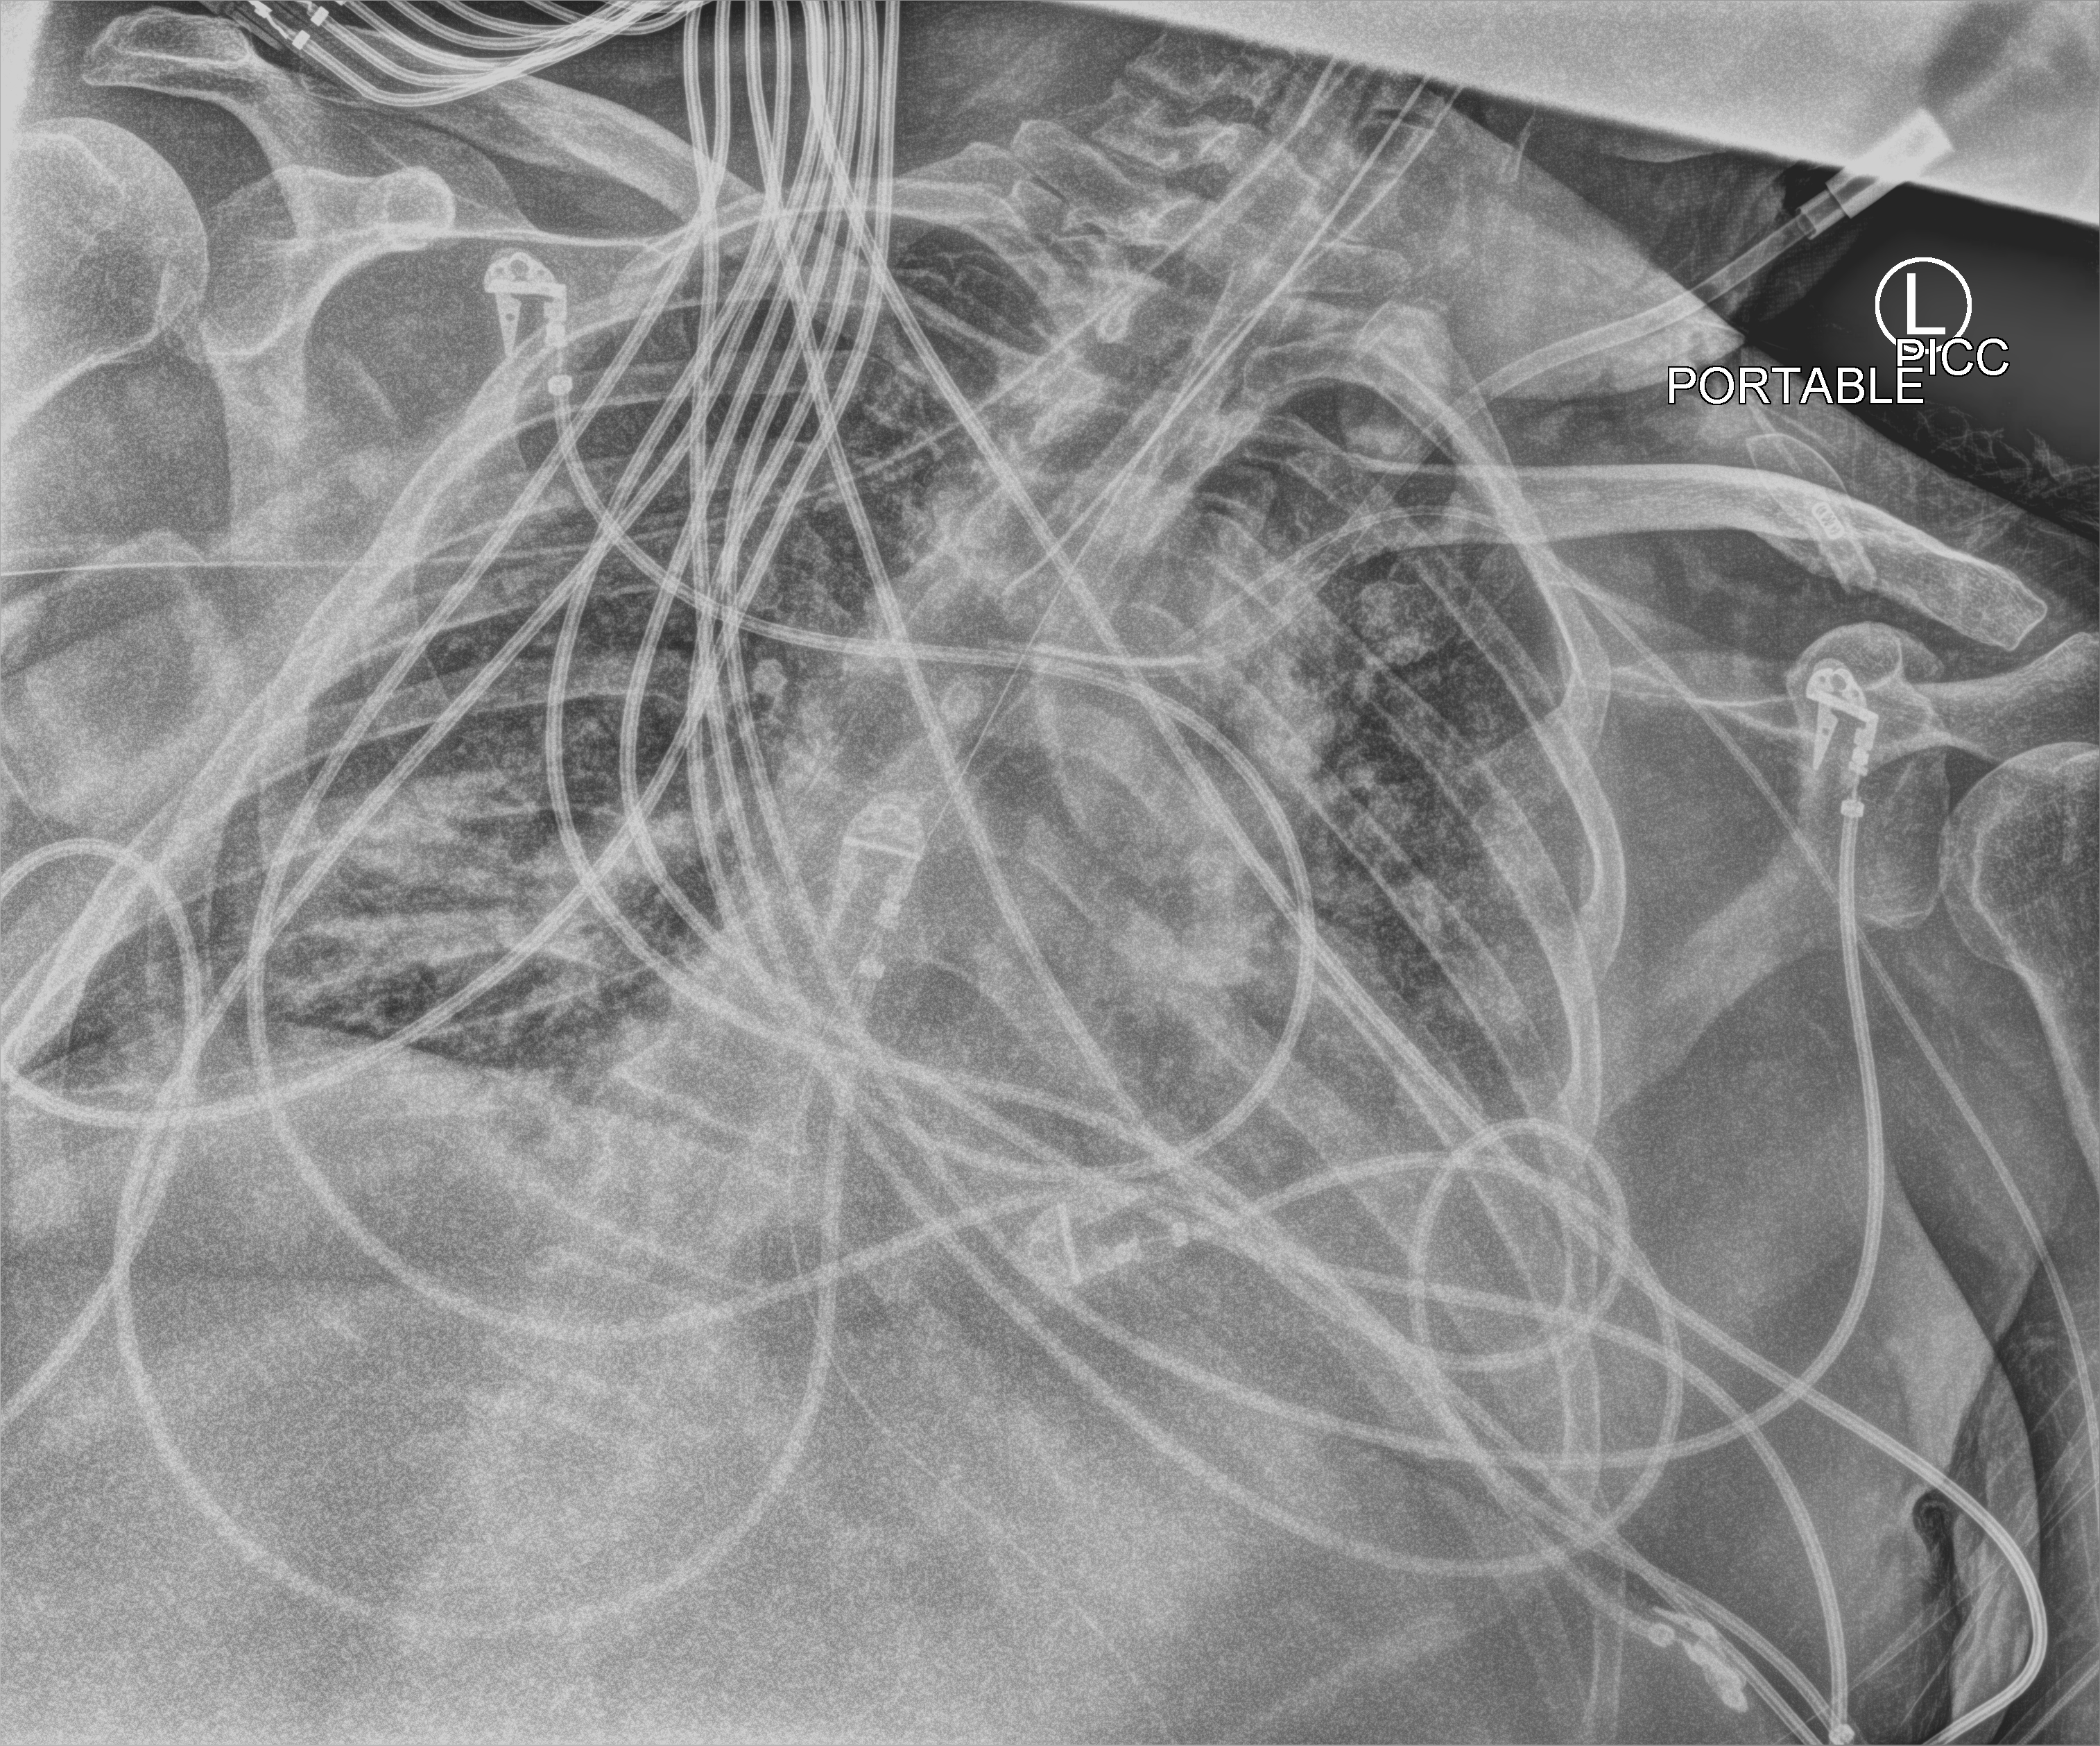
Portable chest radiograph. Male patient hospitalised with COVID-19, age 18–59 years.
Hospital-stay facts (about this admission, not read from this image; timing relative to this image not recorded): diabetes (admission record): no.